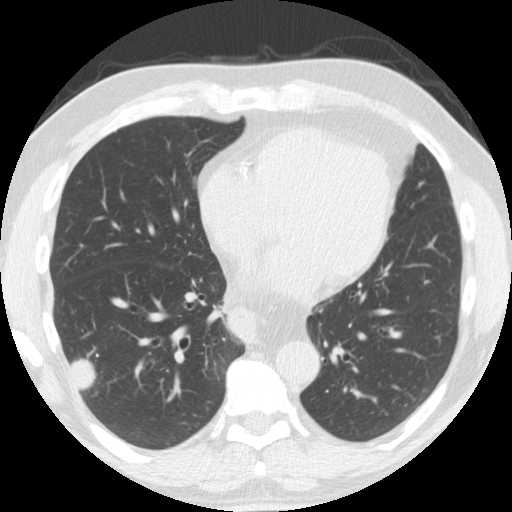
Low-dose screening chest CT, one axial slice. Slice 70 of 174 in the series (ordered by position). Reconstruction kernel STANDARD. Lung window (W 1500 / L -600 HU). 512 × 512 image matrix.
Structures marked on this image (outlined manually by an expert reader):
- lesion 1 (tumor, lower lobe of right lung): box from (x=71, y=359) to (x=96, y=390) px